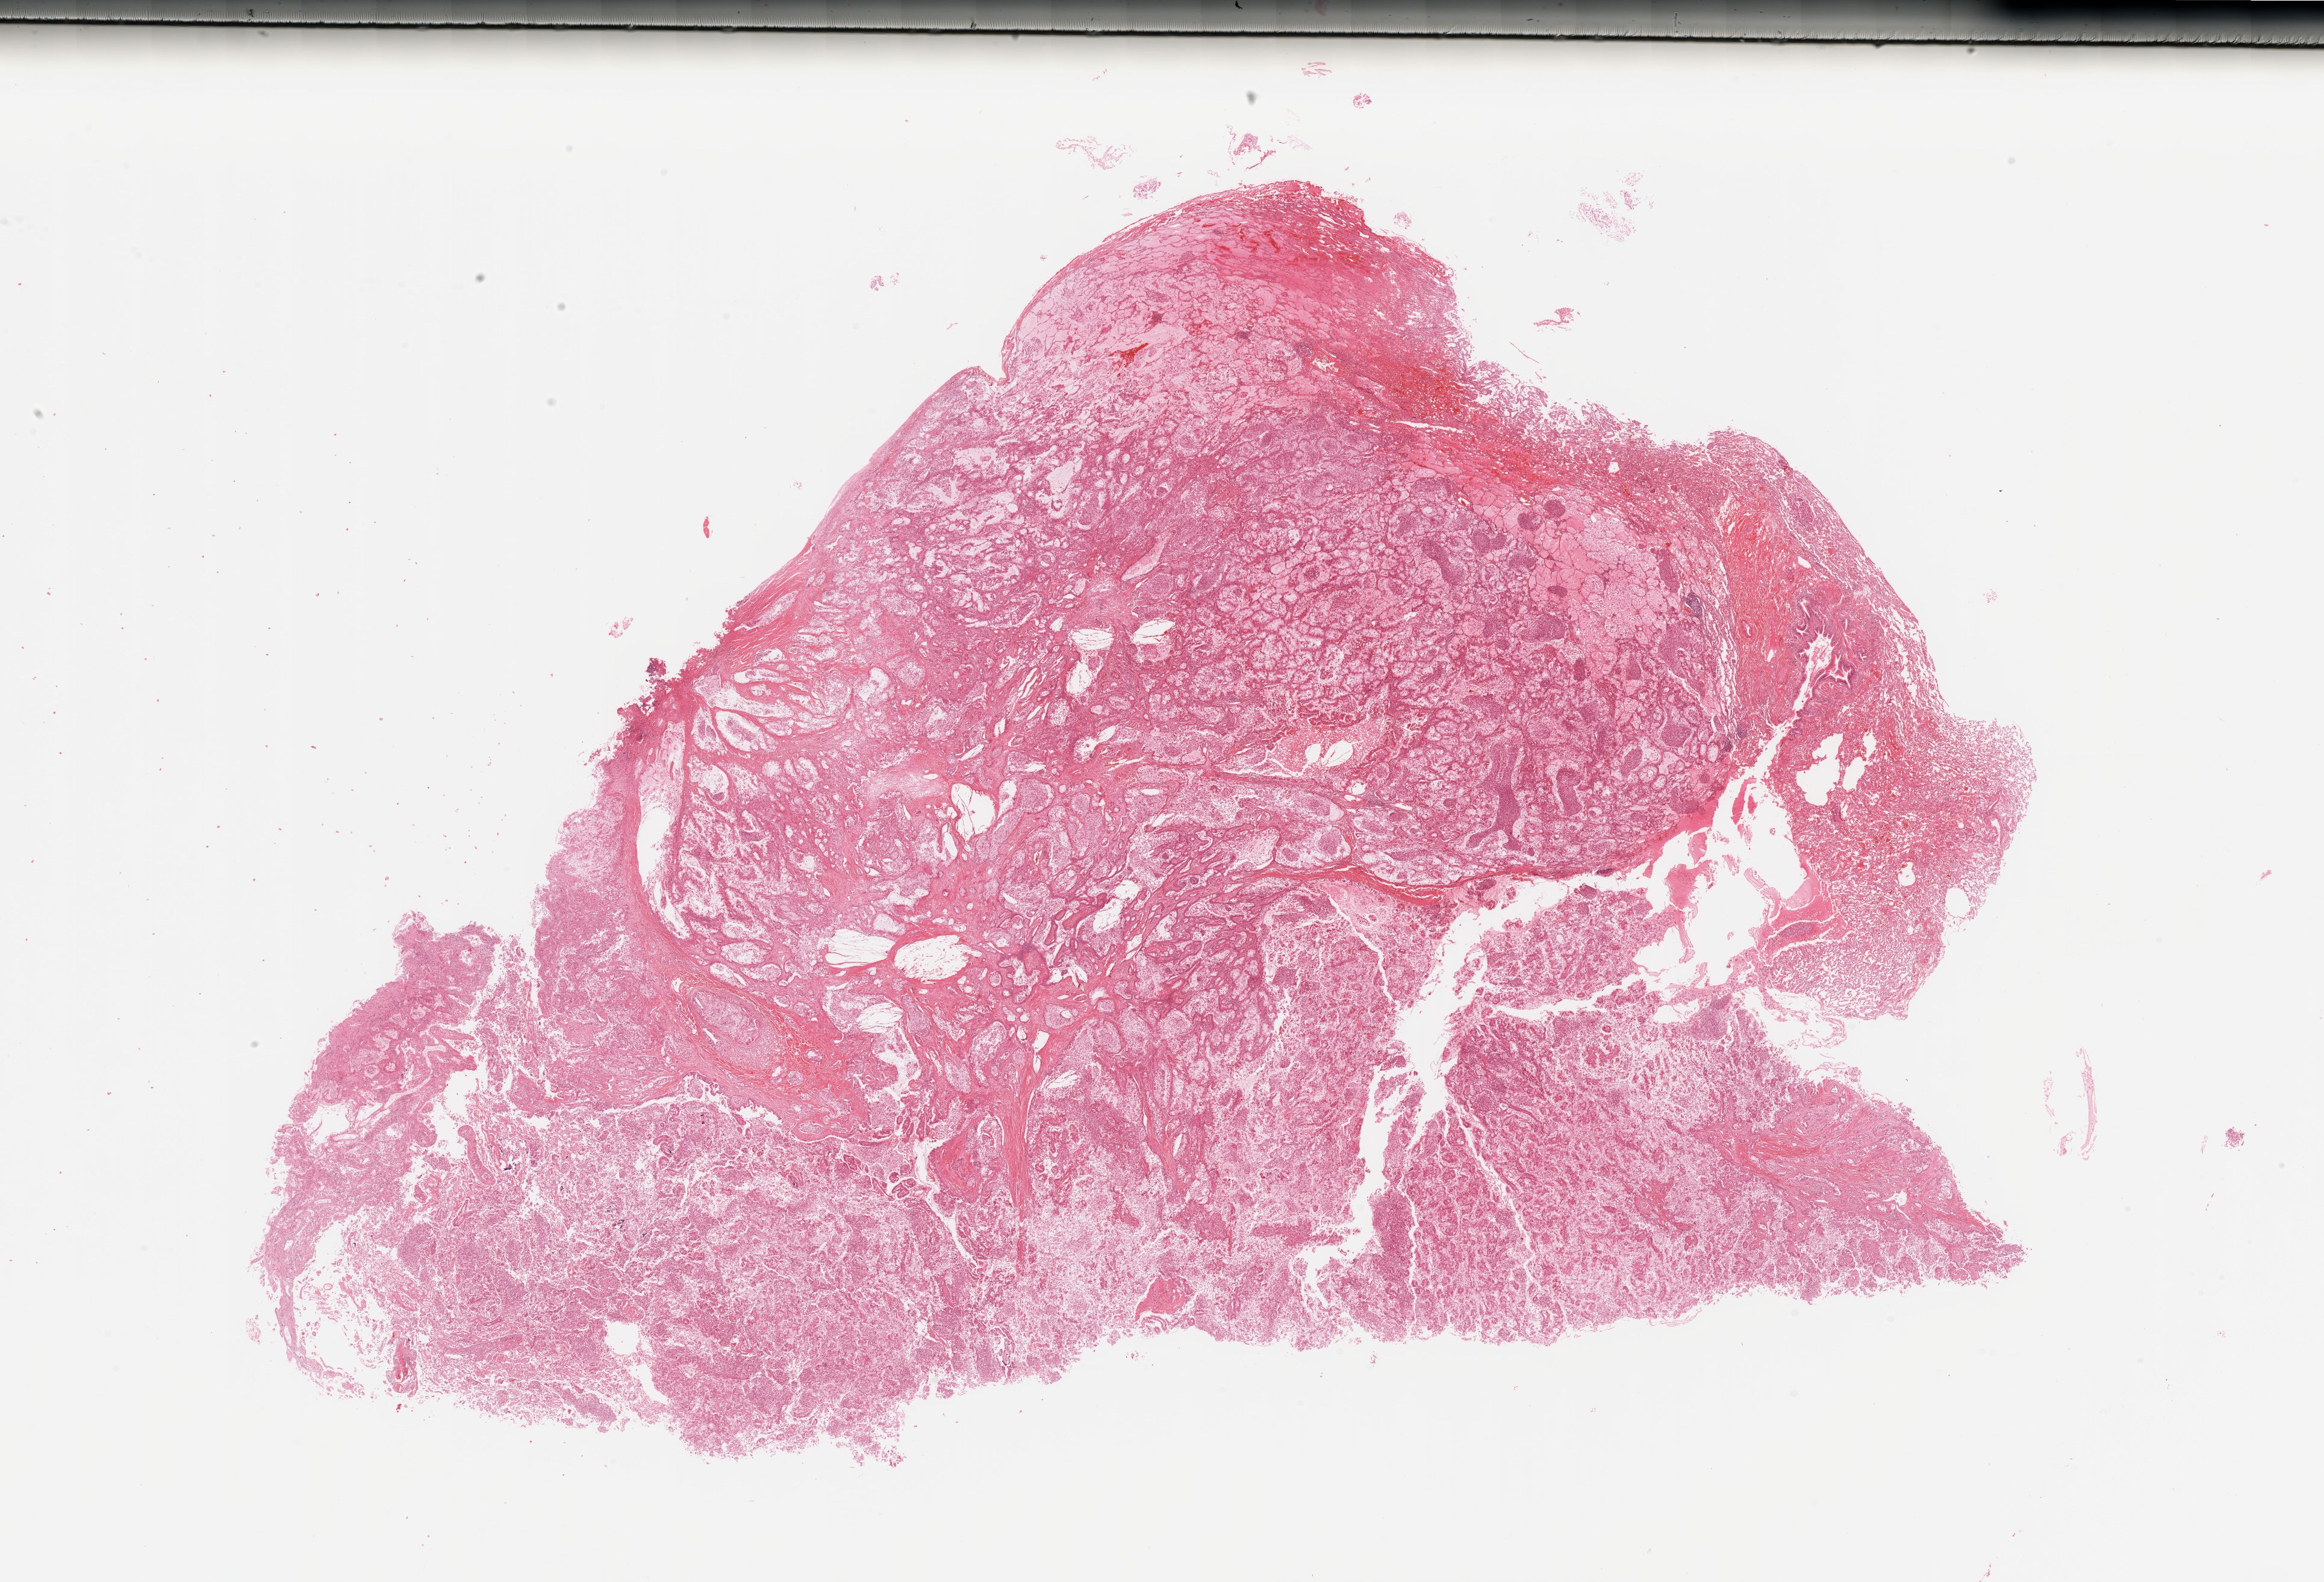
Digitized H&E tissue section (whole slide), shown as a low-resolution overview of the whole scanned area (about 30.5 x 20.8 mm, acquisition: 20x scan); tumour tissue sample, sampled site: lung. Female, 25 y/o. Histologic grade: G2 (moderately differentiated). Pathologist review of this section (percent, as recorded): tumour nuclei 70%, necrosis 3%.
* histologic diagnosis: Adenocarcinoma, NOS